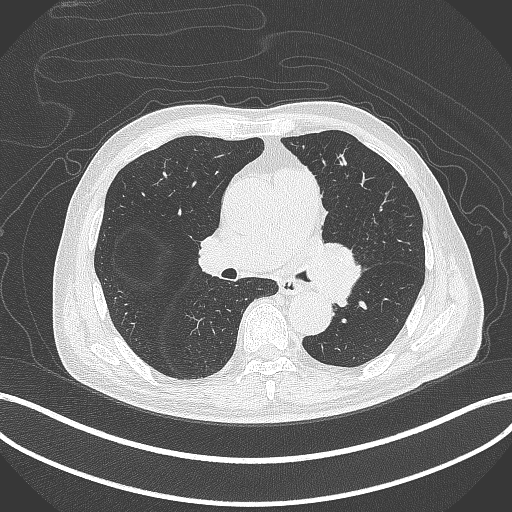
Chest CT, one axial slice. Slice 241 of 417 in the series (ordered by position). 120 kVp. Lung window (W 1500 / L -600 HU). 1 mm slice thickness. 512 × 512 image matrix, field of view 400 × 400 mm. Patient: male, 77 years. Case-level facts recorded for this patient, not image findings: clinical TNM (as recorded): T3 N1 M0.
Outlined on this slice (rectangle marked by the reading radiologist):
- lung tumour (recorded histology: adenocarcinoma): bounding box [x1, y1, x2, y2] px = [306, 236, 364, 308]